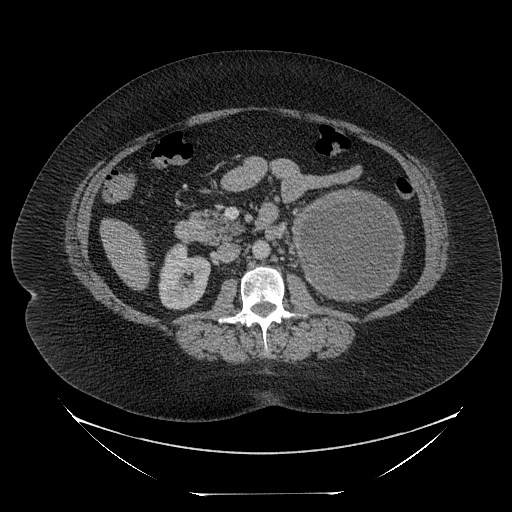
Contrast-enhanced abdominal CT, one axial slice. Position 122 of 205 along the scan axis. 120 kVp. Intravenous contrast given. Soft-tissue window (W 400 / L 40 HU). 512 × 512 image matrix, field of view 500 × 500 mm. Patient: female, 53 years. From the clinical record (not read from this slice): diagnosis: adrenocortical carcinoma; tumour side: left adrenal; tumour size at pathology: 17 cm; Ki-67 index: 20 %; stage (as recorded): 3.
Annotated regions visible in this slice (semi-automatic segmentation, software-assisted and operator-edited):
- mass: box from (x=298, y=192) to (x=402, y=298) px